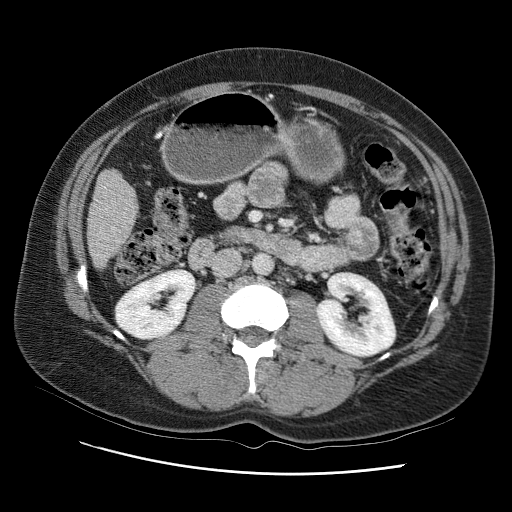
Contrast-enhanced abdominal CT (liver protocol), one axial slice. Slice 25 of 95 in the series (ordered by position). Reconstruction kernel STANDARD. One of 2 acquisitions stored at this slice position. Soft-tissue window (W 400 / L 40 HU). 512 × 512 image matrix, field of view 360 × 360 mm. Case-level facts recorded for this patient, not image findings: diagnosis: hepatocellular carcinoma (patient treated with transarterial chemoembolisation; whether this scan precedes or follows treatment is not stated here); TNM stage (as recorded): Stage-I; Child-Pugh class: B.
Outlined on this slice (semi-automatic segmentation, software-assisted and operator-edited):
- liver parenchyma outside the tumour (the mass and vessels are separate outlines, so this box may not span the whole liver): box from (x=88, y=152) to (x=148, y=268) px
- liver vessels: (x=107, y=196)–(x=124, y=216)